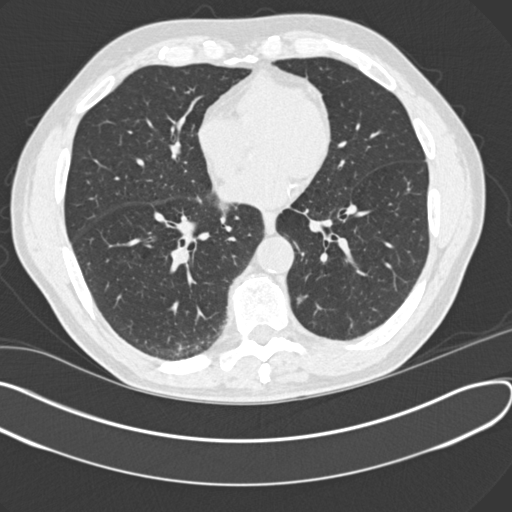
Low-dose screening chest CT, one axial slice. Slice 69 of 166 in the series (ordered by position). Reconstruction kernel B30f. Lung window (W 1500 / L -600 HU). 512 × 512 image matrix.
Annotated regions visible in this slice (expert manual segmentation):
- lesion 1 (tumor, lower lobe of left lung): bounding box (x1, y1, x2, y2) in pixels: (296, 293, 308, 306)